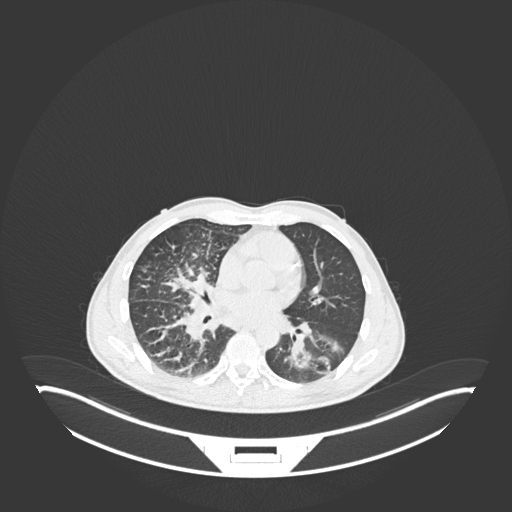
Chest CT, one axial slice; position 115 of 237 along the scan axis; reconstruction kernel B30f; 120 kVp; lung window (W 1500 / L -600 HU); 512 × 512 image matrix. Patient: male, 49 years. From the clinical record (not read from this slice): clinical TNM (as recorded): T2b N1 M0.
Annotated regions visible in this slice (bounding box drawn by a radiologist):
- lung tumour (recorded histology: adenocarcinoma): box from (x=290, y=324) to (x=348, y=375) px